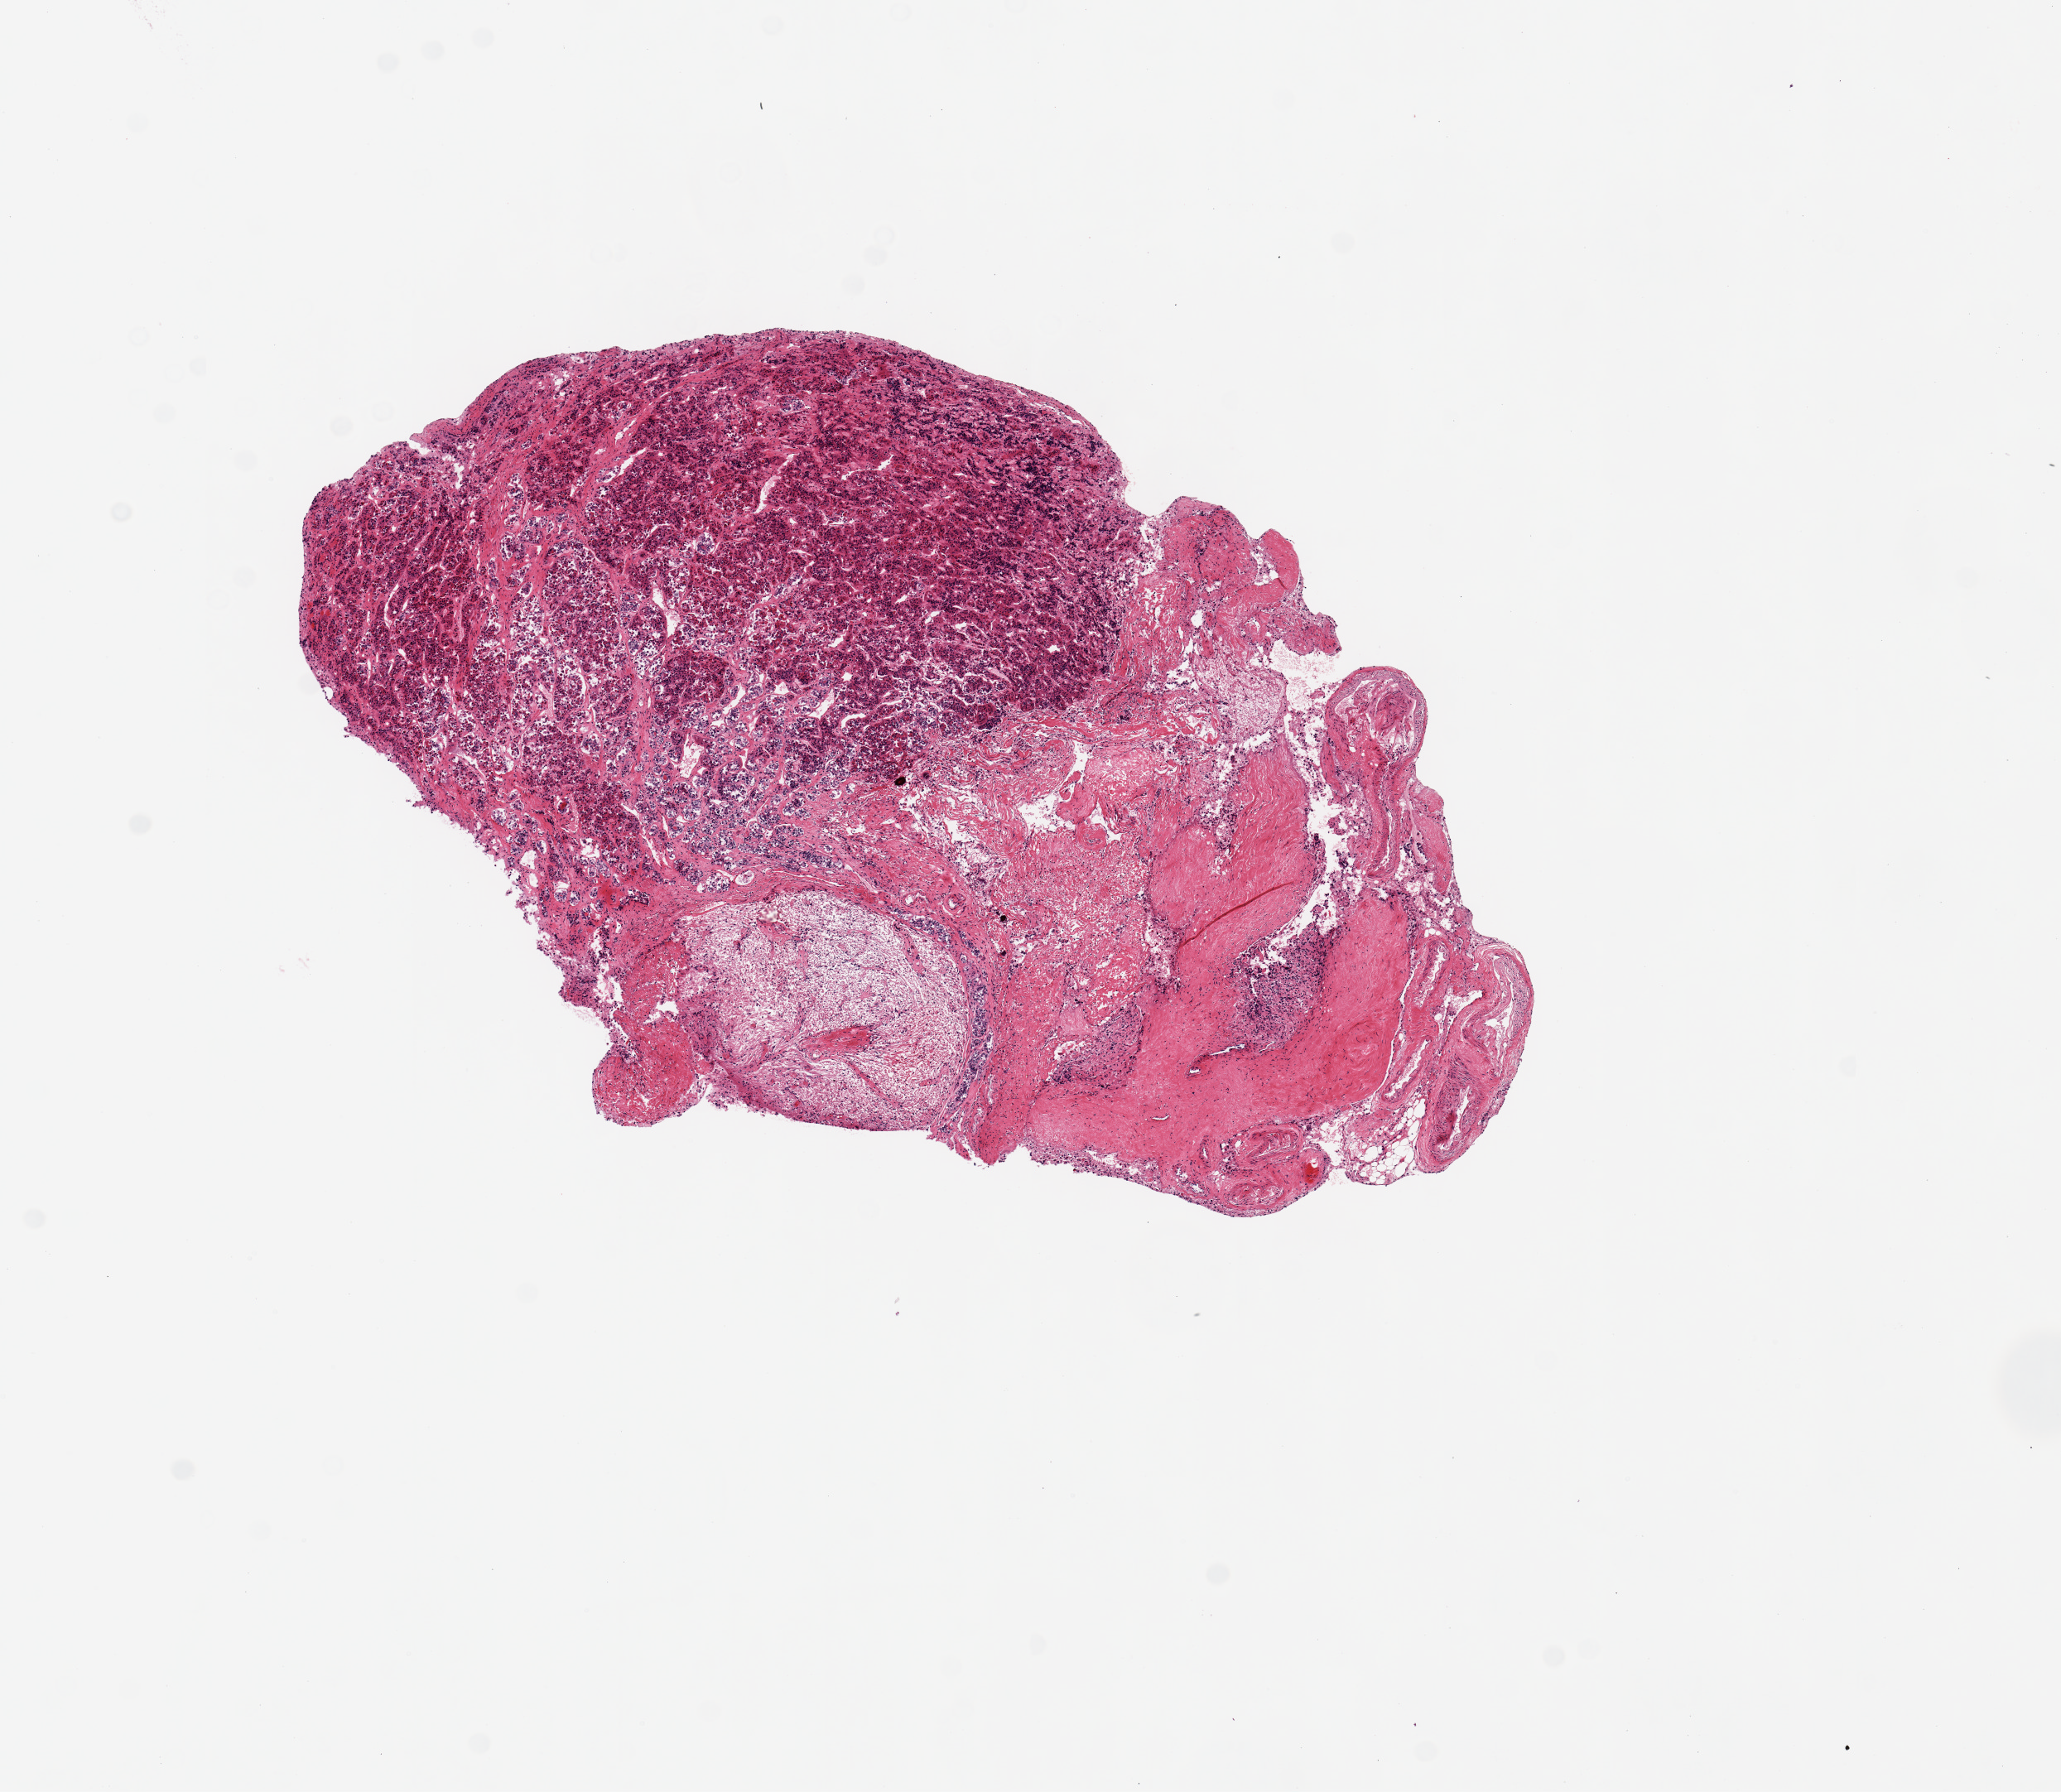
Hematoxylin and eosin (H&E) whole-slide image — shown as a low-resolution overview of the whole scanned area (about 9.8 x 8.6 mm, slide scanned at 20x). PAXgene-fixed paraffin-embedded (PFPE) section. Sampled site (target tissue): pituitary. Tissue donor sample. Donor sex: male.
Pathologist's review note for this sample: 1 piece, moderately autolyzed.